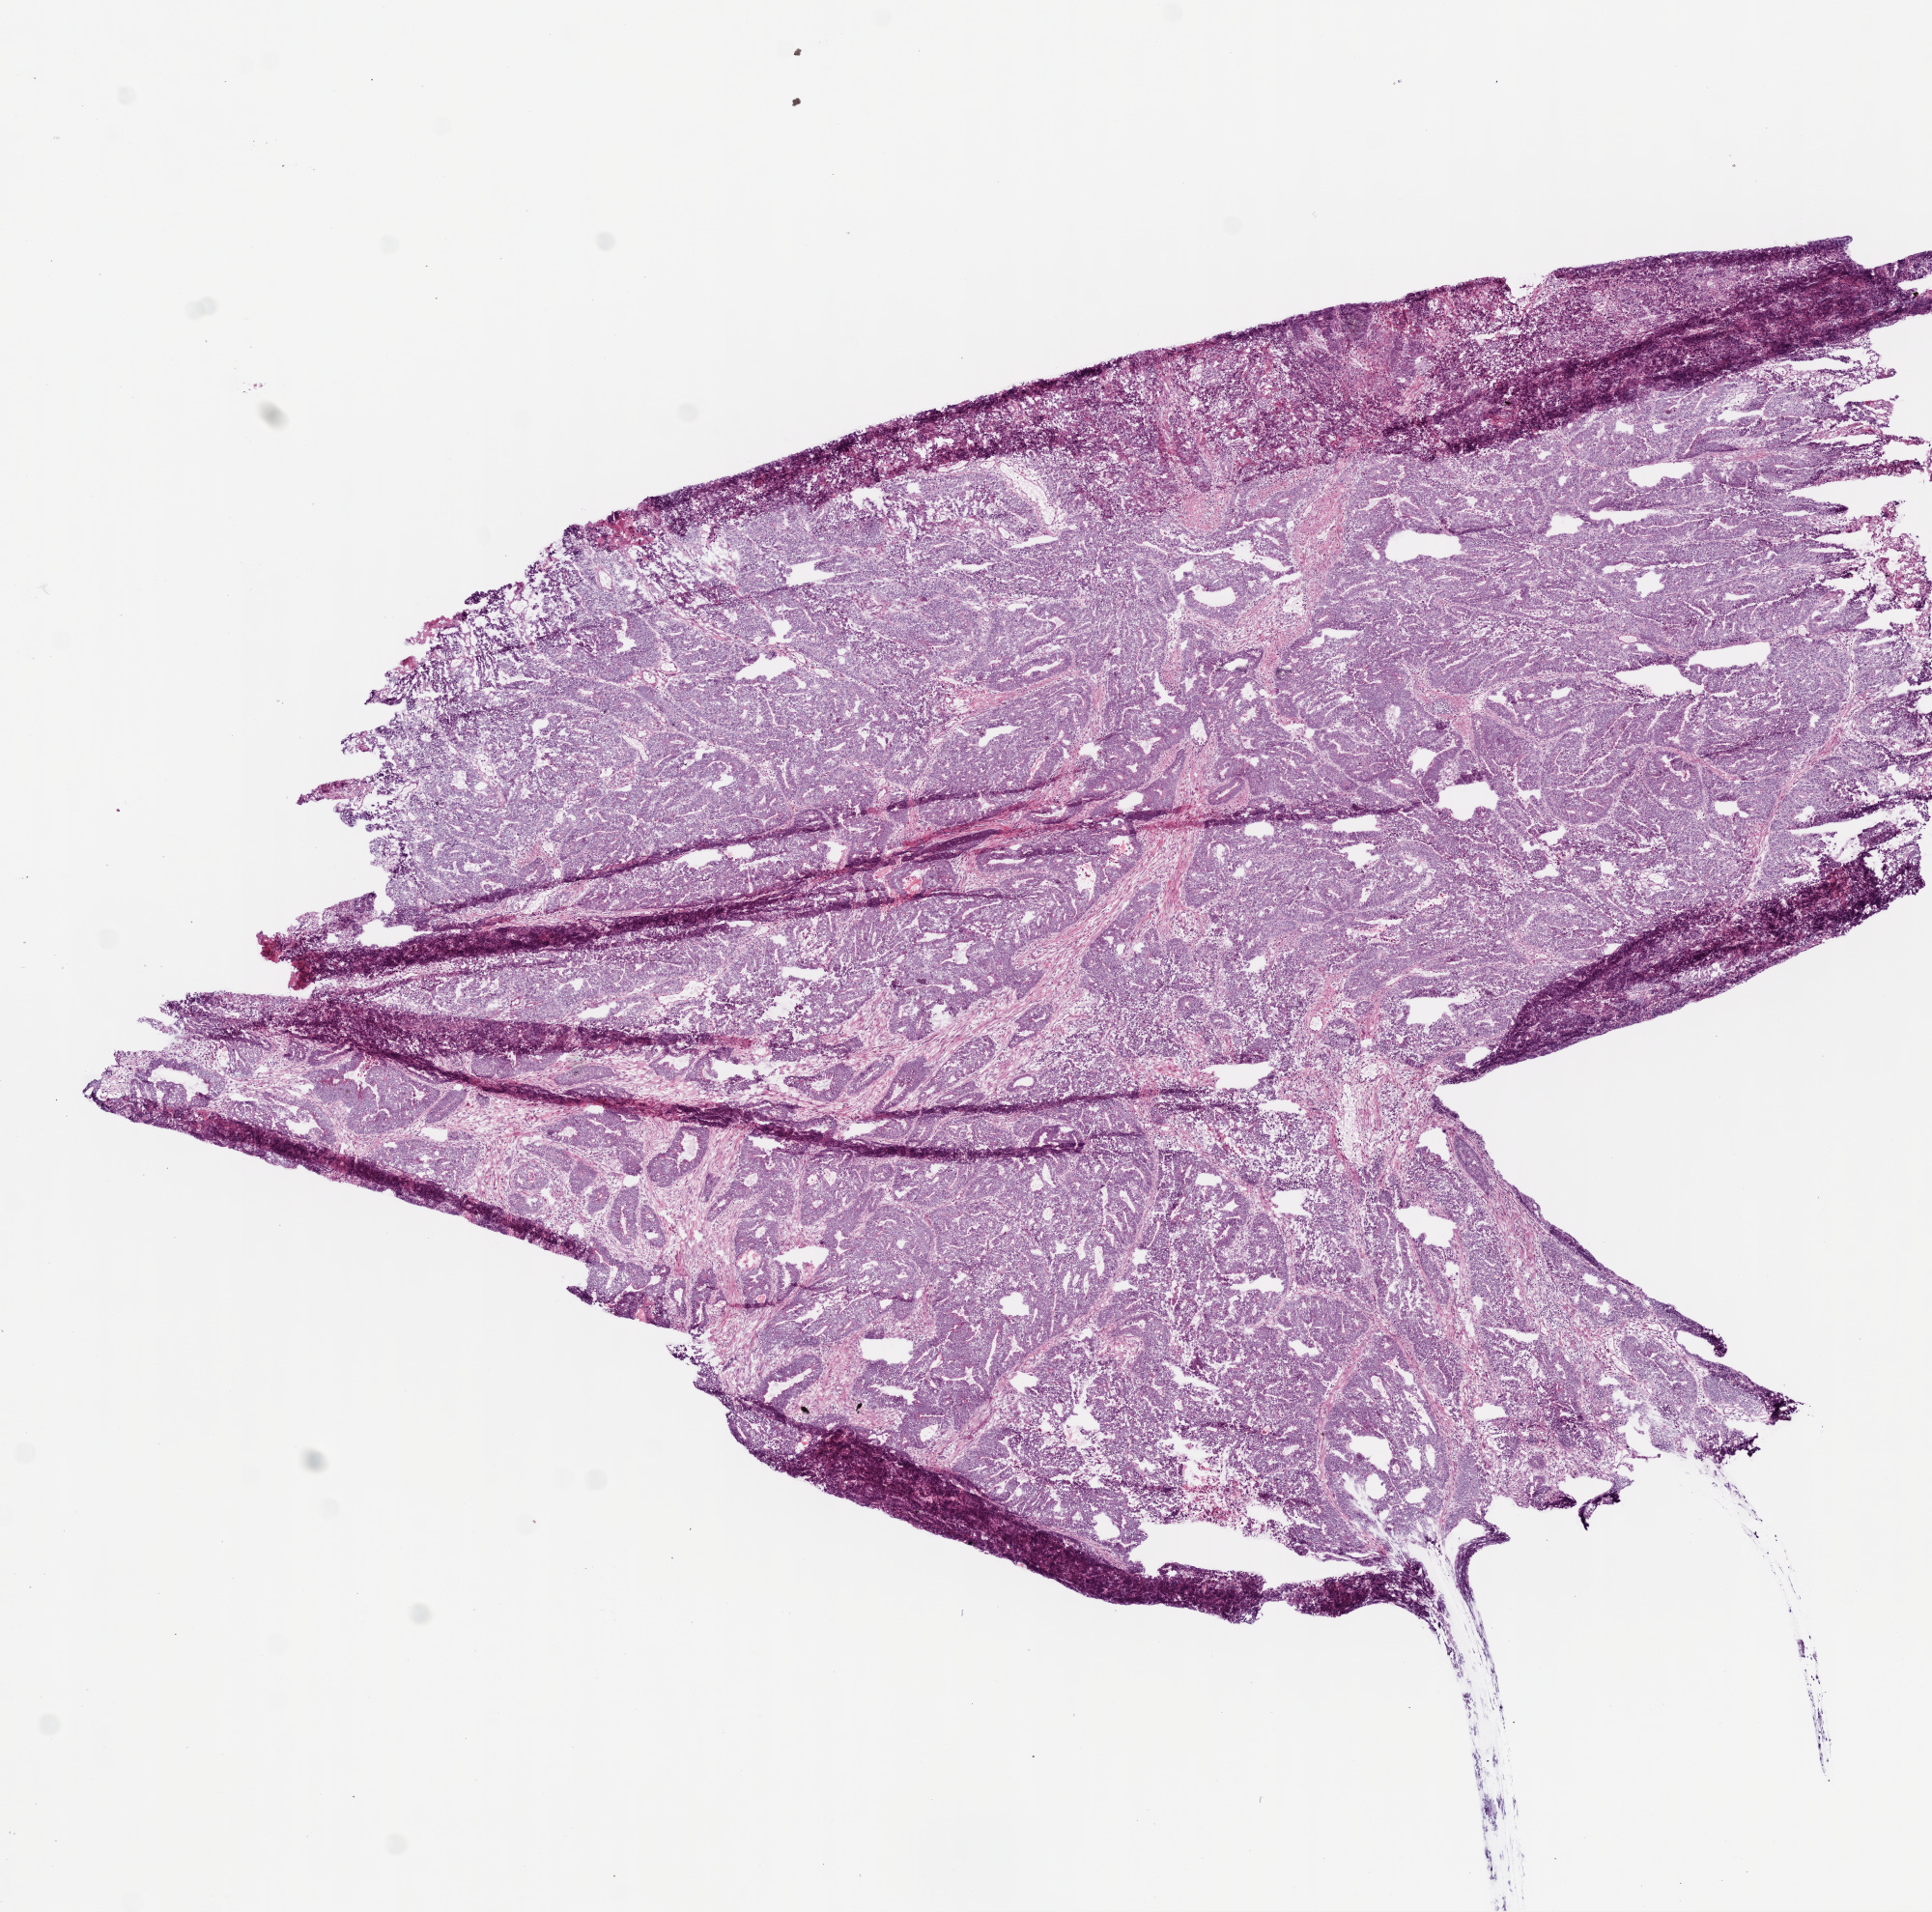
Digitized Hematoxylin and eosin (H&E) stained tissue section (whole slide) — a low-resolution overview of the entire scanned area, about 8.0 x 7.9 mm (acquisition: 20x scan), frozen section, sample: primary tumour, rectum. Male, age 68 years at initial diagnosis. Composition of this section per pathologist review: tumour cells 88%, tumour nuclei 80%, normal cells 0%, stromal cells 5%, necrosis 8%.
- histologic diagnosis: Mucinous adenocarcinoma
- AJCC pathologic stage: IIA (6th edition)
- lymph nodes positive (case pathology): 0 of 14 examined